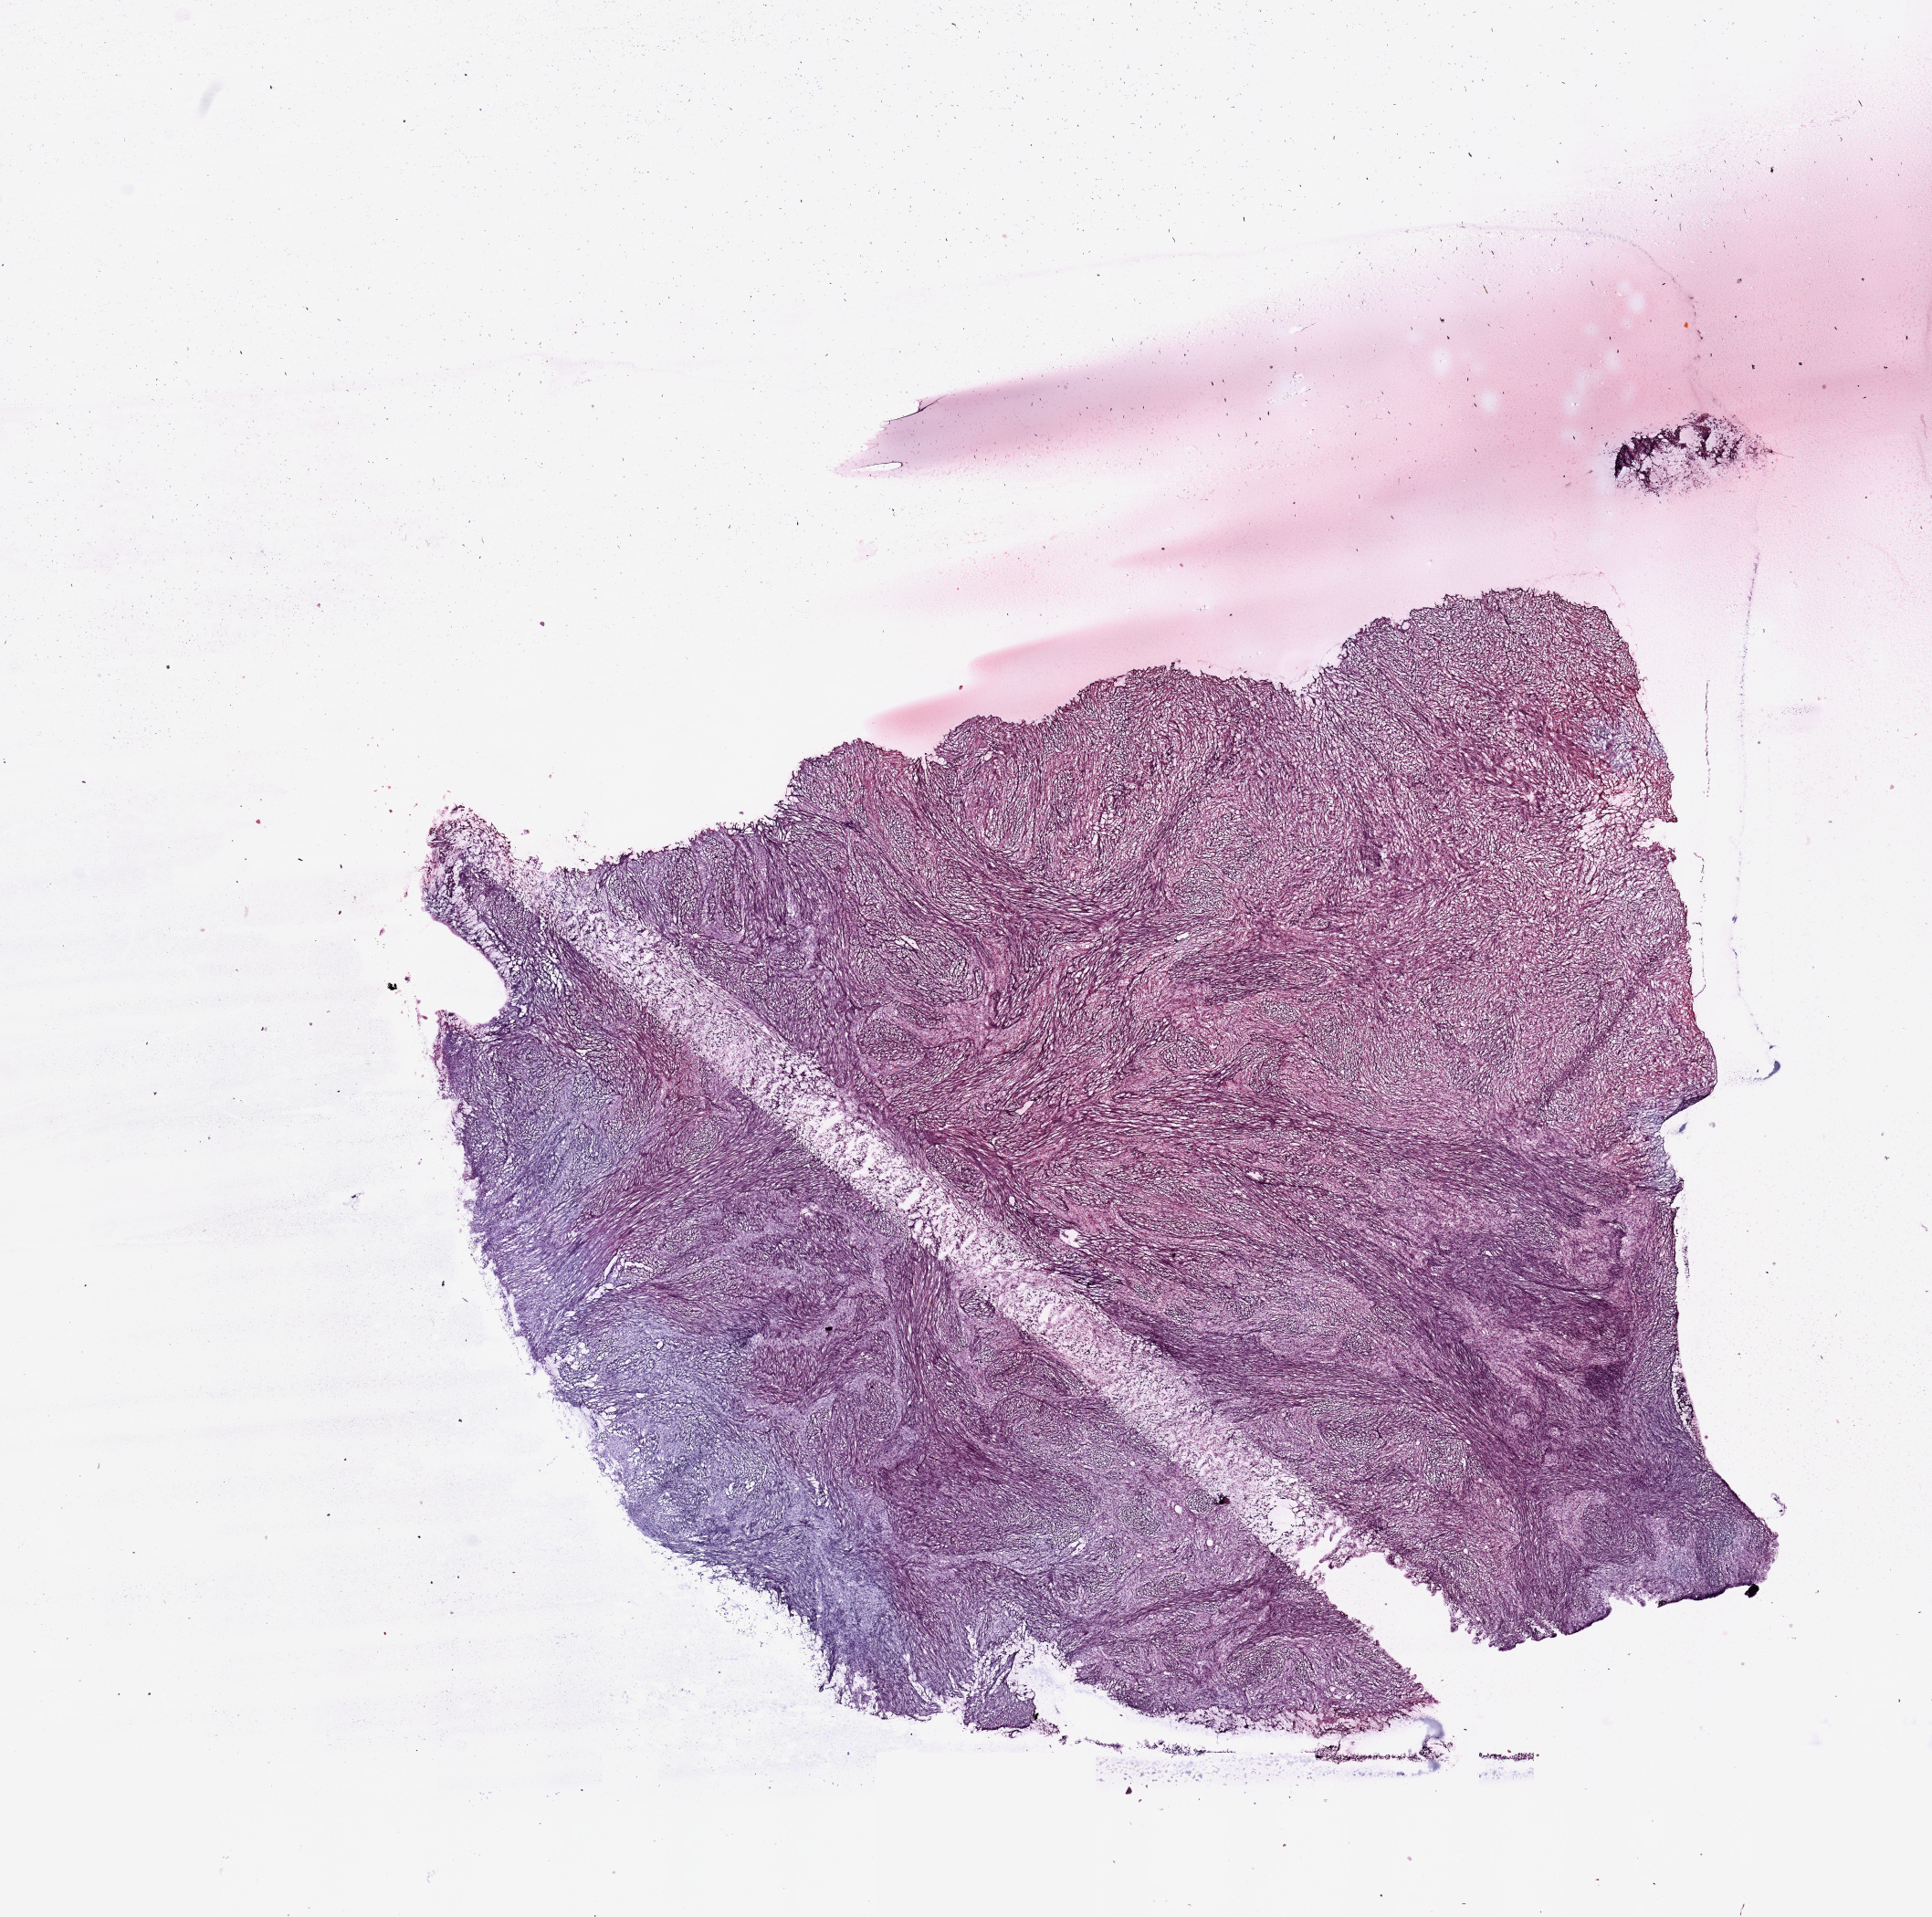
Digitized H&E tissue section (whole slide), whole scanned area (about 16.7 x 16.6 mm) shown as a low-resolution overview; tumour tissue sample. 42-year-old female patient.
Primary tumour site (as recorded): chest. Patient diagnosis (cohort enrolment): sarcoma (site not recorded at cohort level).